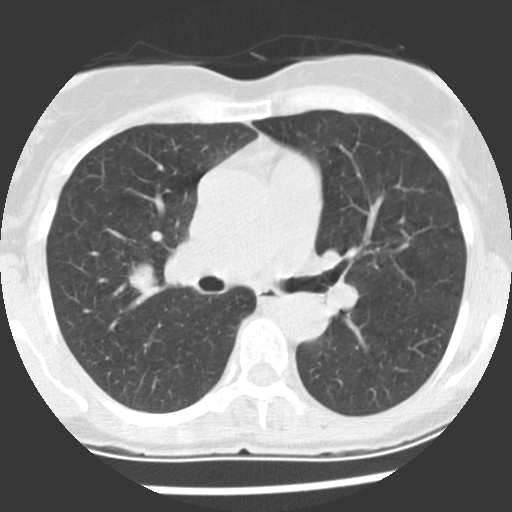
Axial slice from a low-dose chest CT screening exam, baseline annual screen, lung window (W 1500 / L -600 HU), 2.5 mm slice thickness, standard (soft-tissue) reconstruction kernel (STANDARD), 120 kVp, 512 × 512 image matrix, field of view 270 × 270 mm. Female participant, aged 60 years at enrolment. Current smoker at enrolment.
Expert reader's lesion annotation, bounding box [x1, y1, x2, y2] px = [115, 257, 171, 304]. The screening reader recorded 2 non-calcified nodules or masses ≥4 mm on this exam; which of them this box marks is not recorded. Later outcome: lung cancer diagnosed 10 days after this screen — adenocarcinoma, NOS, right upper lobe, stage IIIA (AJCC 6th edition), 20 mm at pathology.